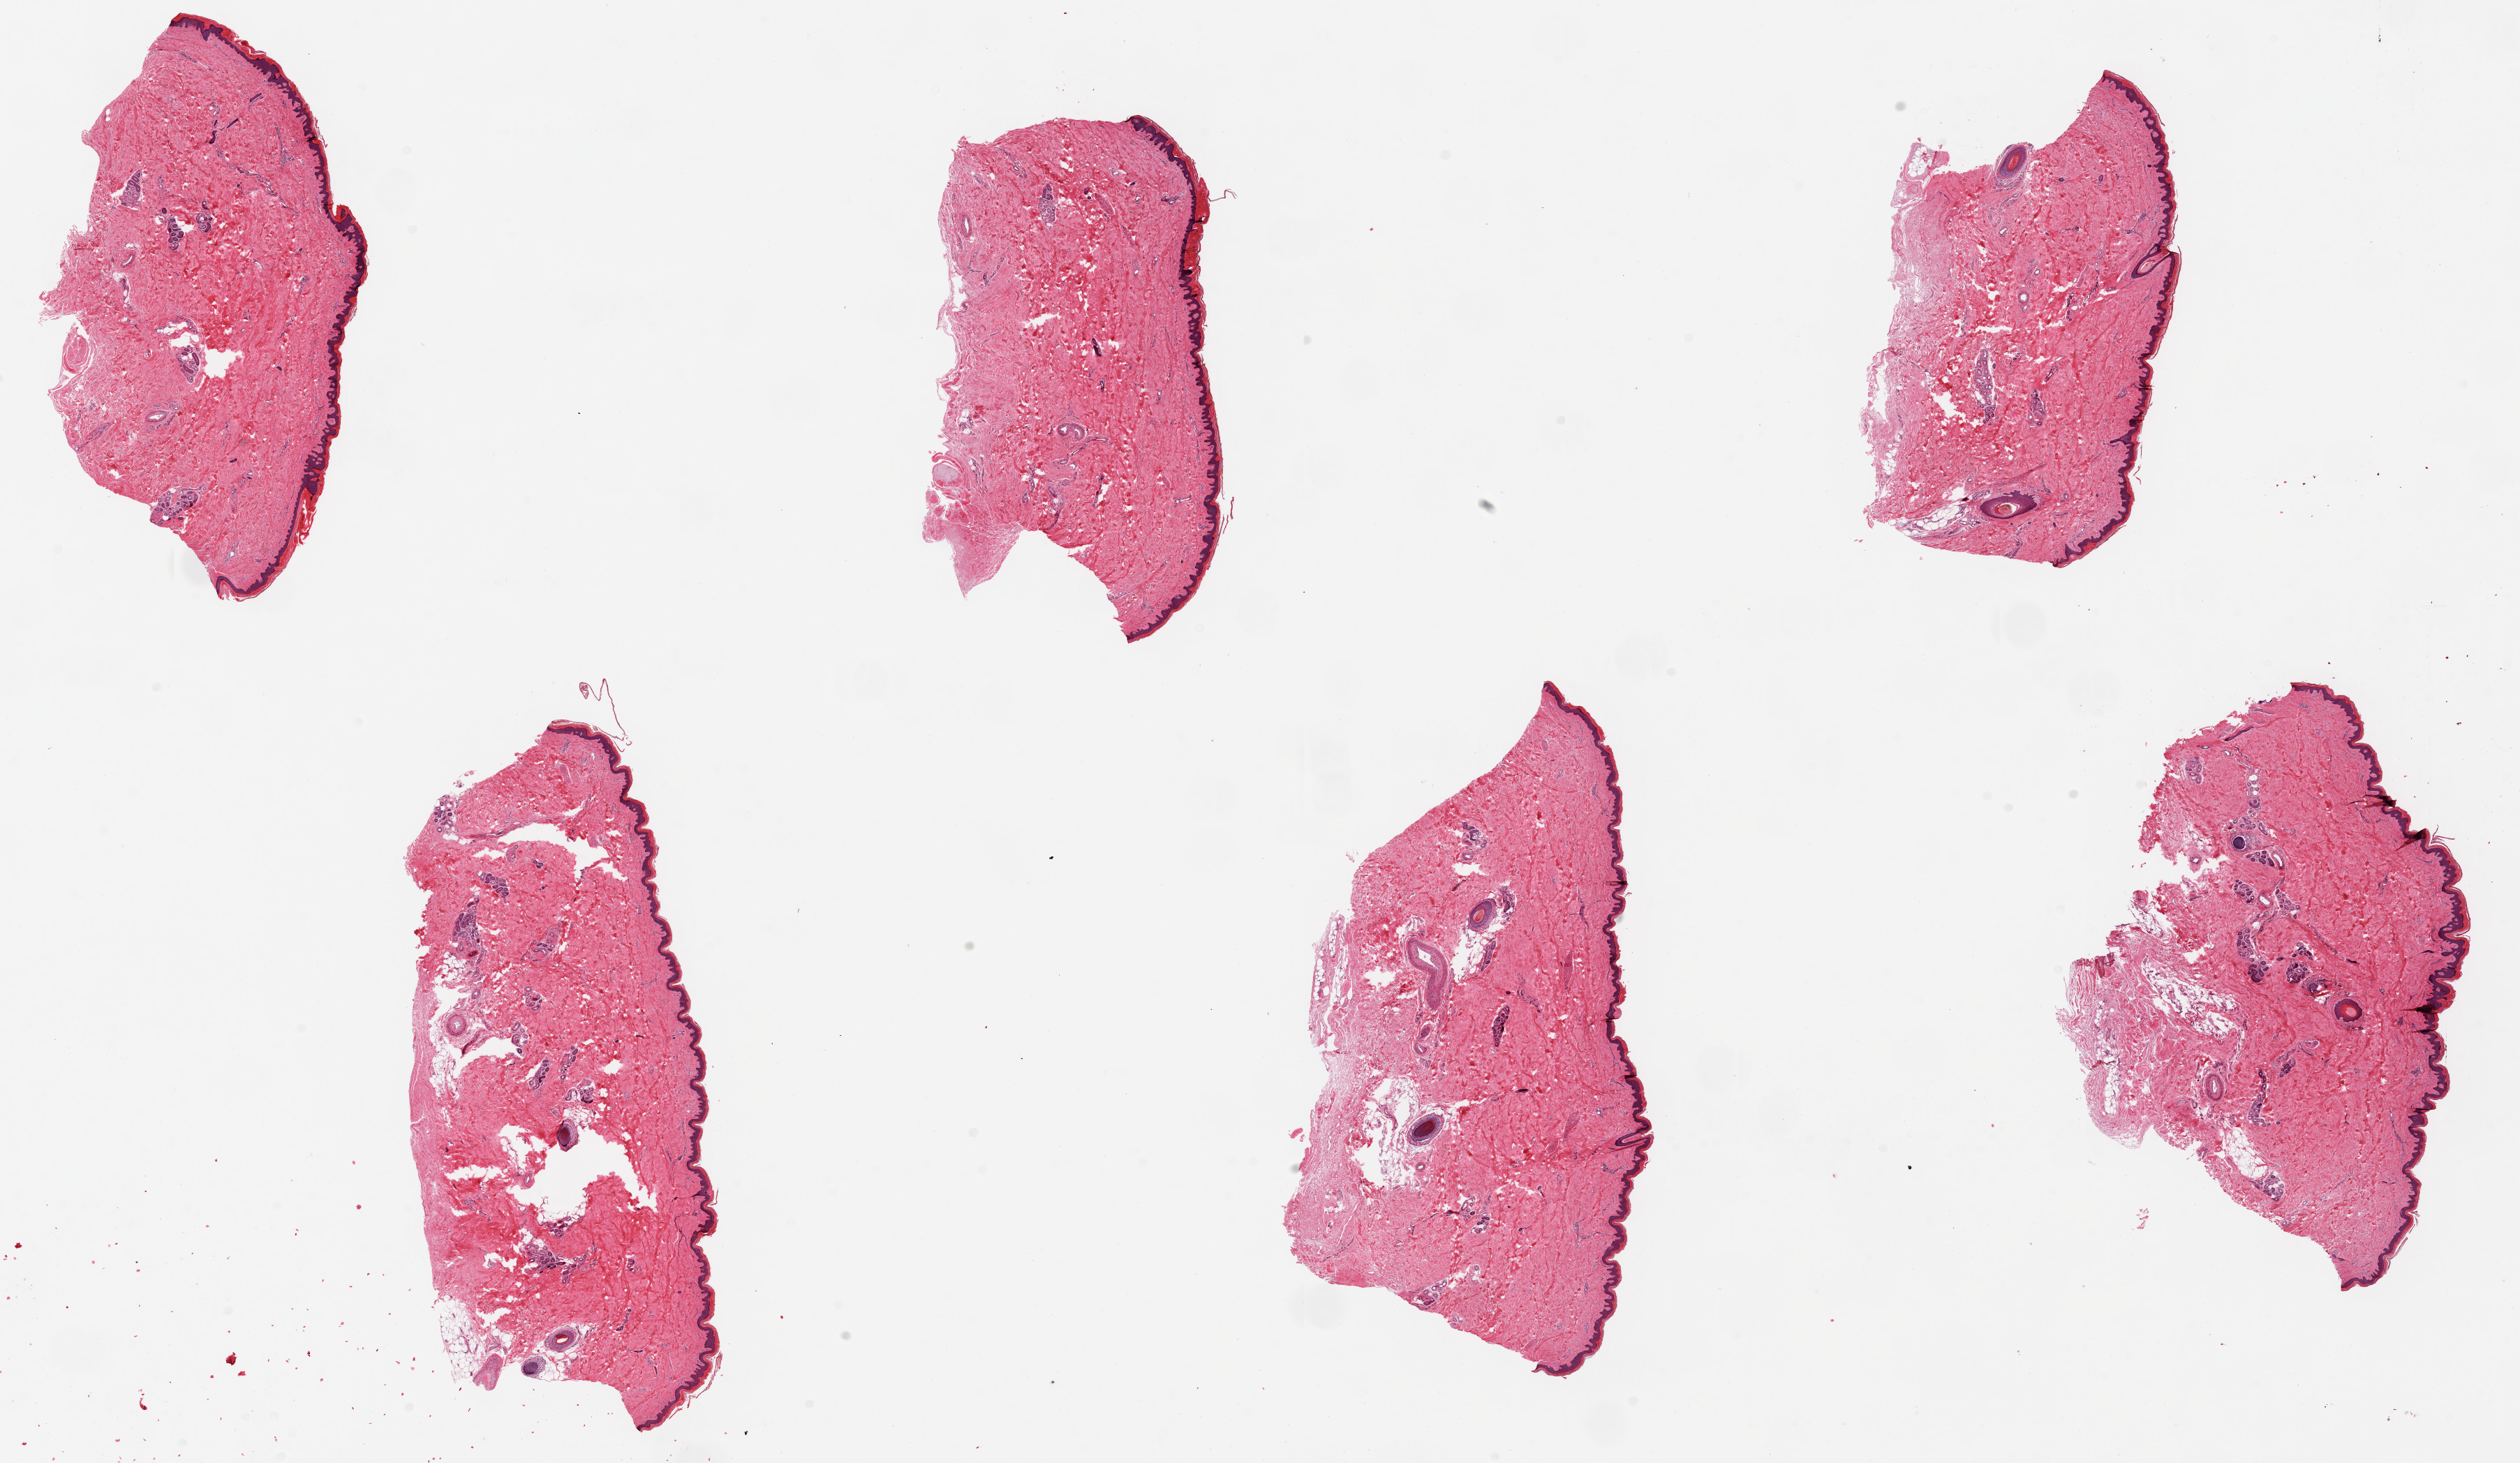
Digitized haematoxylin and eosin-stained section, brightfield — a low-resolution overview of the entire scanned area, about 28.5 x 16.6 mm; PAXgene-fixed paraffin-embedded (PFPE) section; target tissue: skin of lower leg; donor tissue sample. Donor sex: male.
• reviewer comment on this tissue sample: 6 pieces, up to 8x3.5mm; squamous epithelium is ~2% thickness